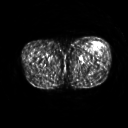
FDG PET of an extremity soft-tissue mass (from a PET/CT study), one axial slice. Position 218 of 267 along the scan axis. 3.27 mm slice thickness. 128 × 128 image matrix, field of view 500 × 500 mm. Male patient, age 64 years. Case-level facts recorded for this patient, not image findings: histological type: extraskeletal osteosarcoma; grade: high; site of the primary tumour: thigh.
Outlined on this slice (expert contour drawn on MRI and transferred to this co-registered scan by the dataset authors):
- gross tumour volume (mass): box from (x=95, y=44) to (x=100, y=51) px